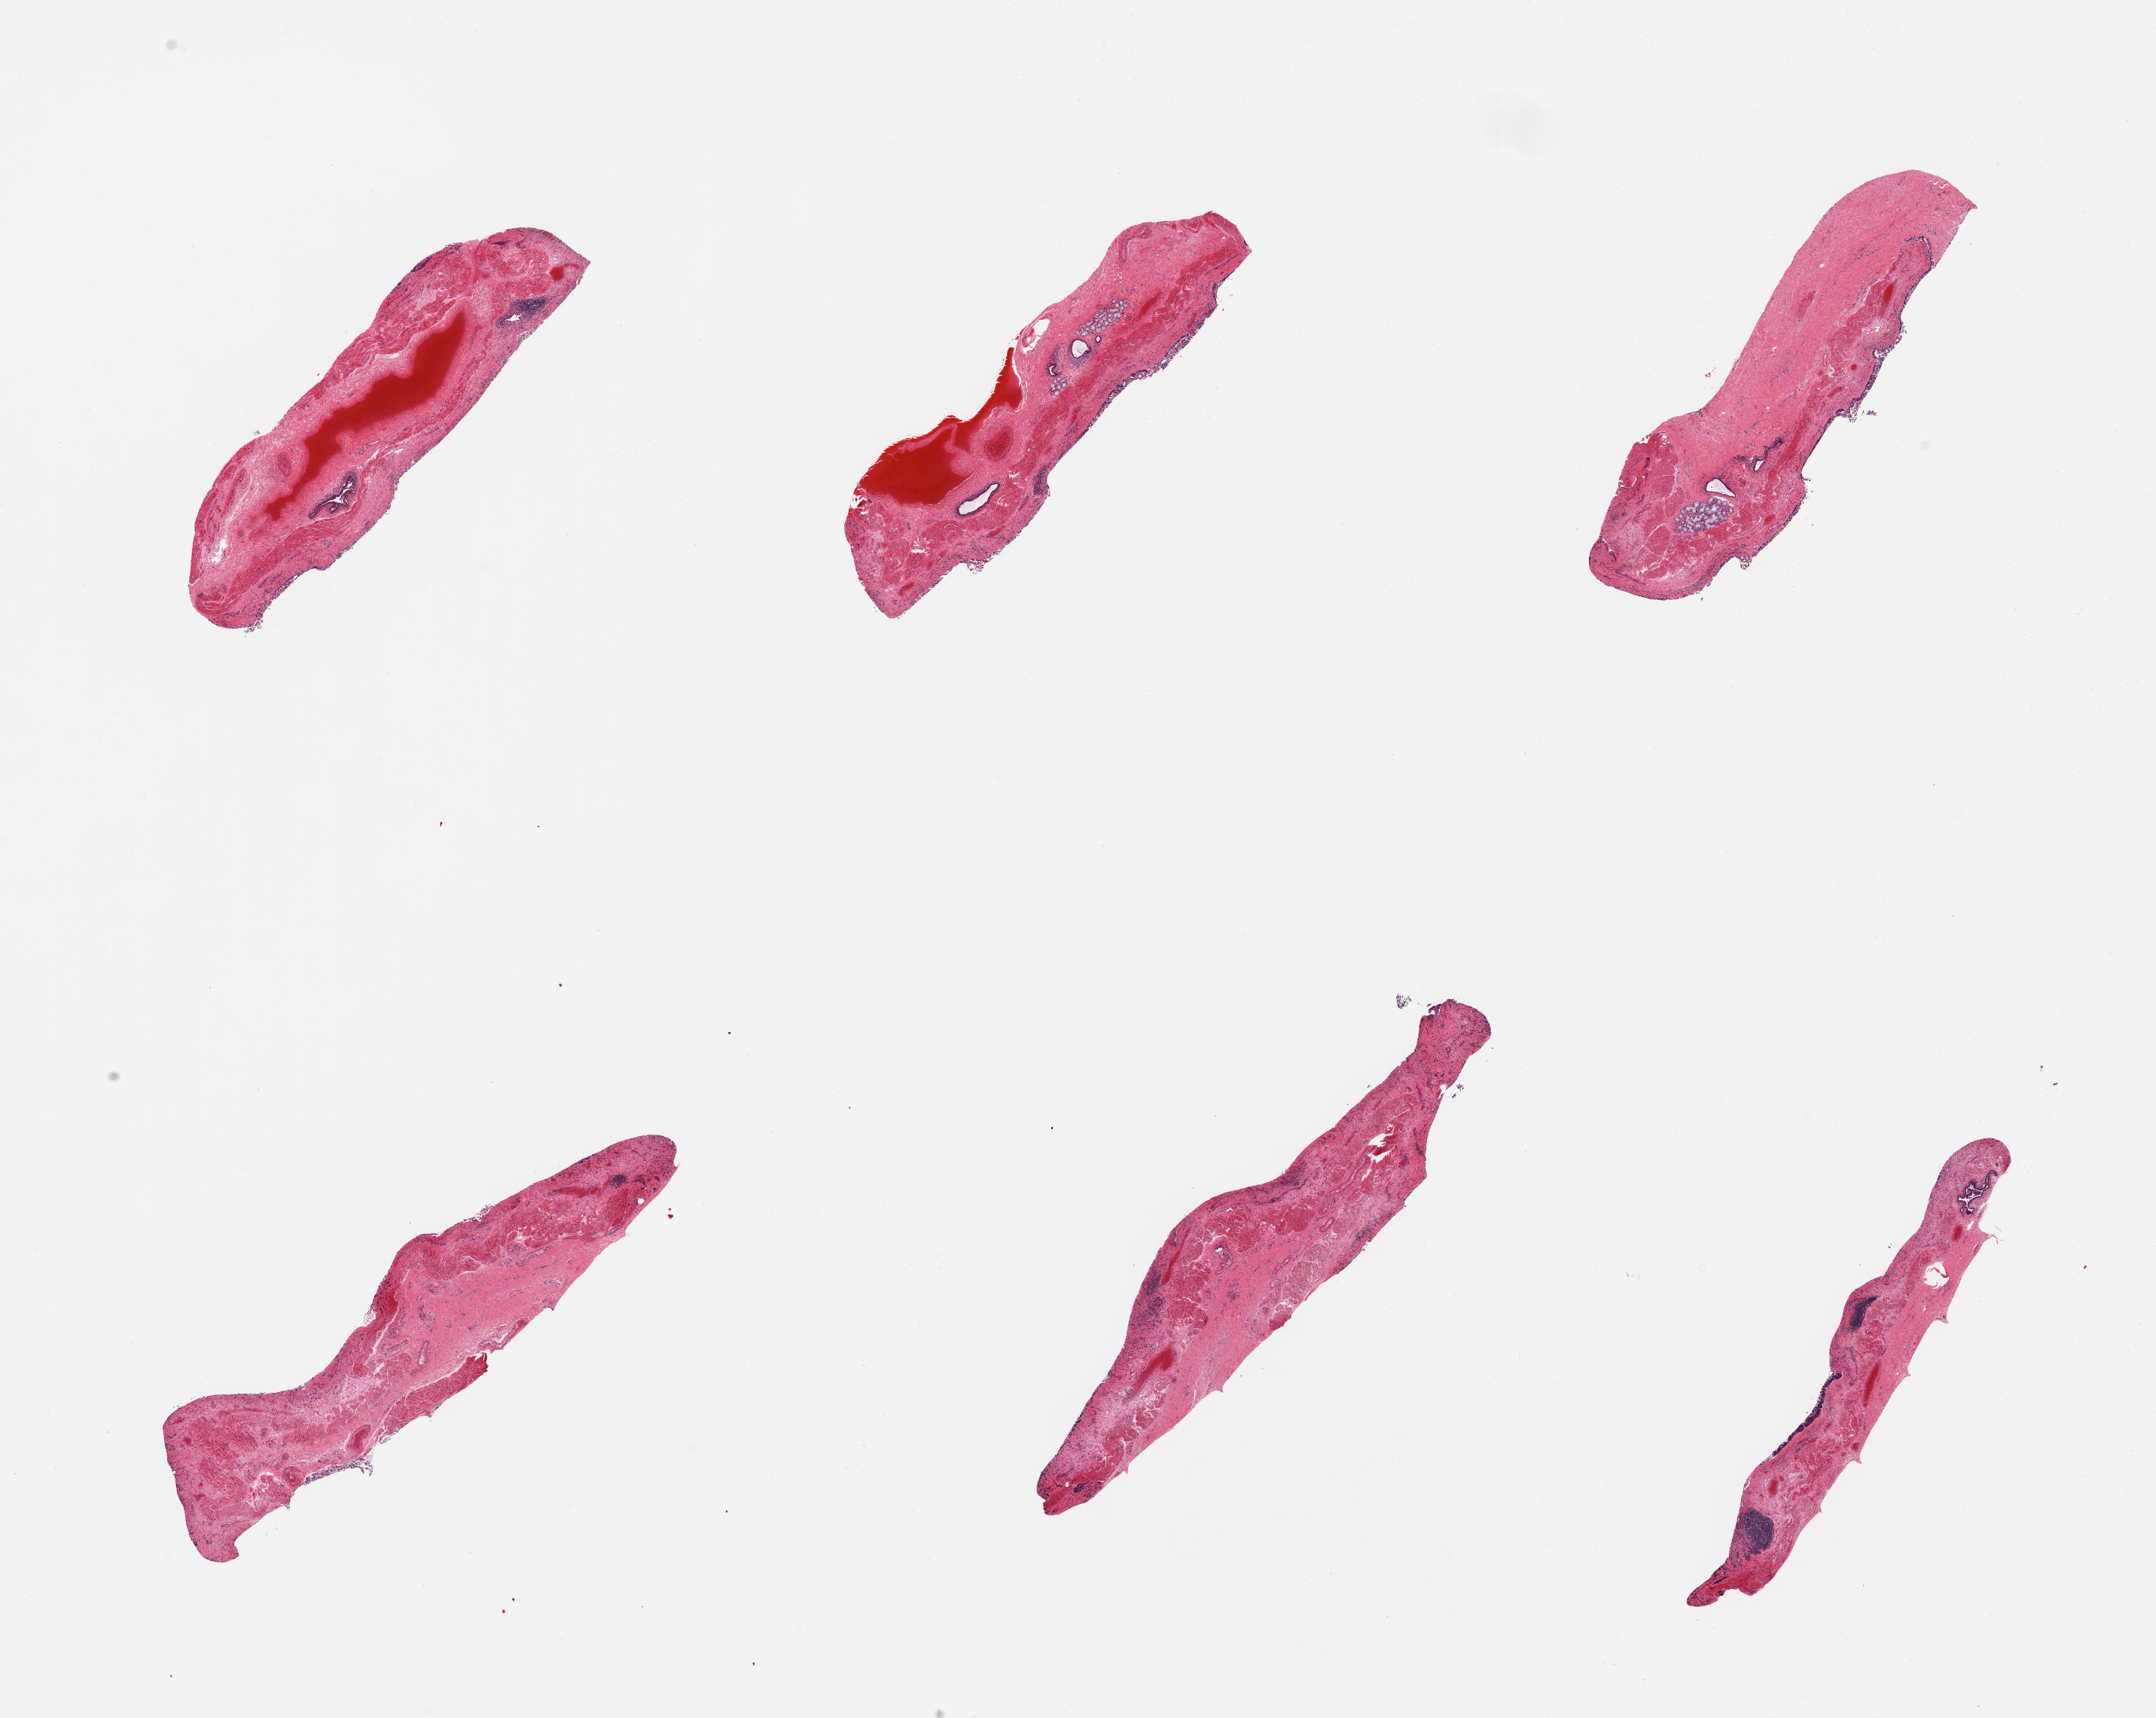
Whole-slide image, hematoxylin and eosin (H&E) stain, whole scanned area (about 22.6 x 18.0 mm) shown as a low-resolution overview; PAXgene-fixed, paraffin-embedded tissue; target tissue: esophageal mucous membrane; tissue donor sample. Donor: male.
Review note (as recorded): 6 pieces, epithelium predominantly sloughed, some submucosal glands and dilated ducts.